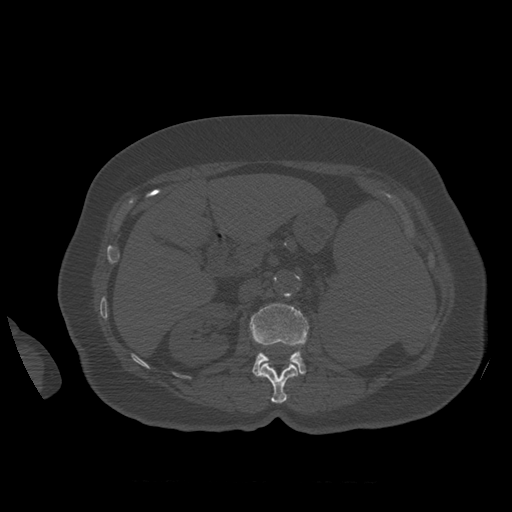
CT including the spine, one axial slice. Slice 265 of 399 in the series (ordered by position). Reconstruction kernel STANDARD. Bone window (W 1800 / L 400 HU). 1.25 mm slice thickness. 512 × 512 image matrix, field of view 404 × 404 mm. Patient age 81 years. Case-level facts recorded for this patient, not image findings: primary cancer: renal; vertebrae with lytic lesions (as recorded): L1.
Outlined on this slice (semi-automatically segmented with operator editing):
- L1 vertebra: bounding box (x1, y1, x2, y2) in pixels: (259, 363, 298, 404)
- L2 vertebra: (250, 303, 309, 377)